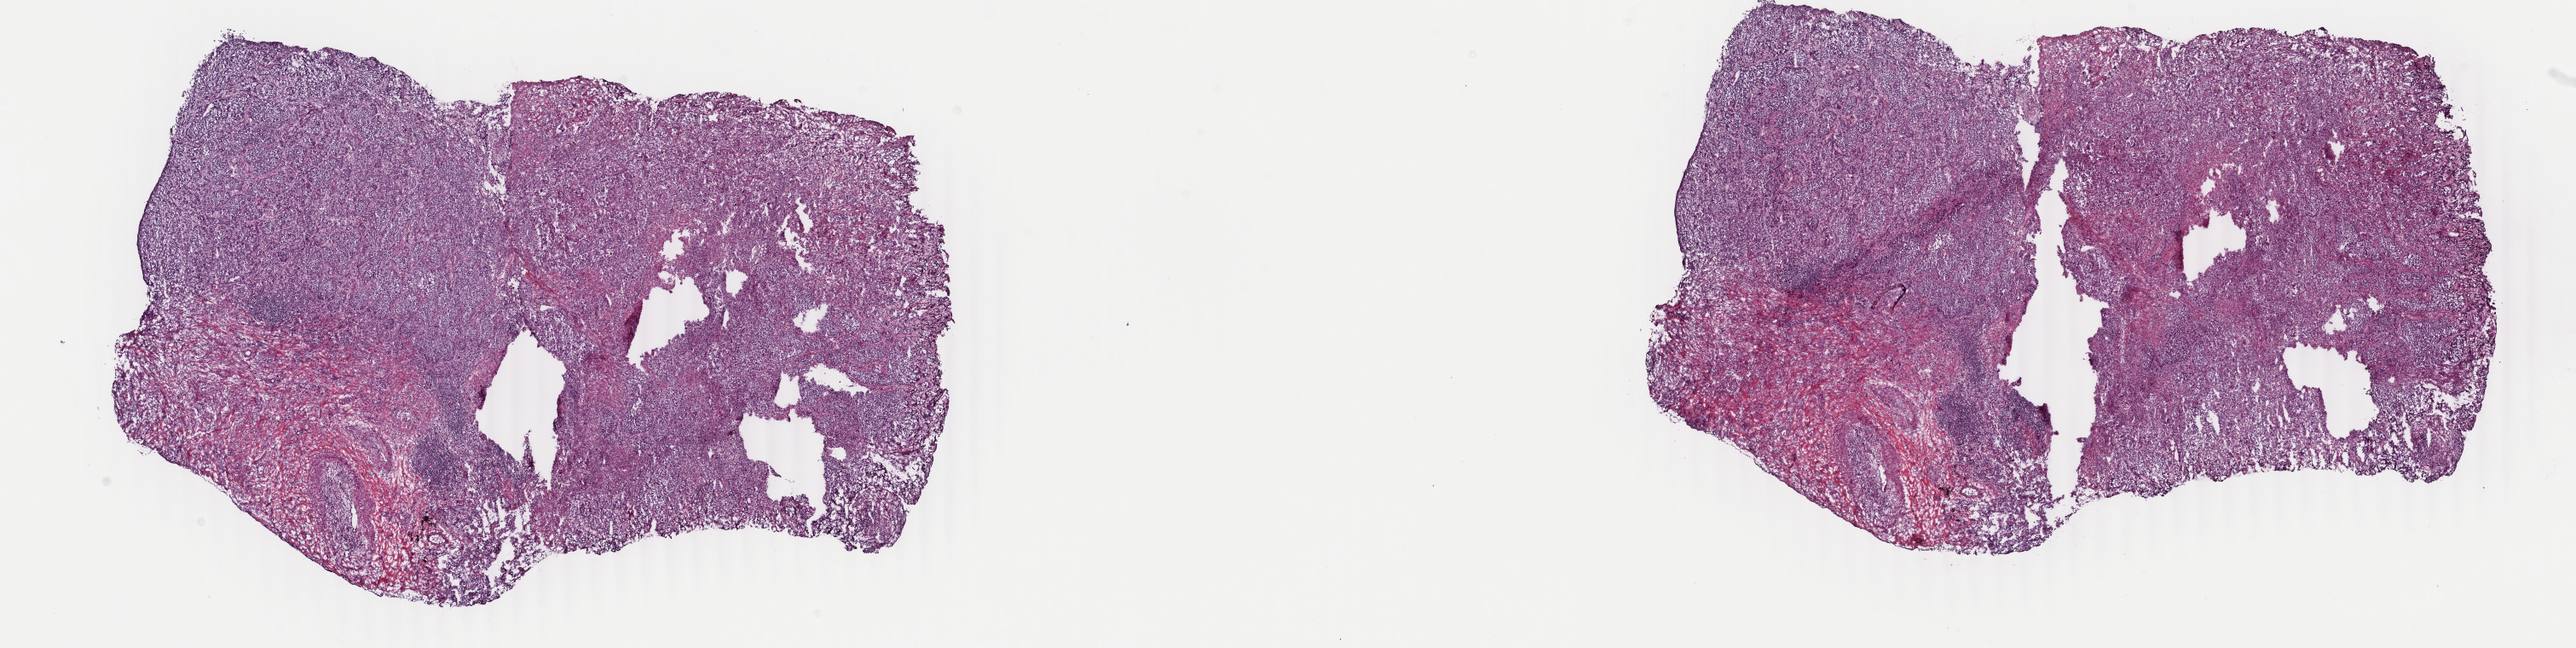
Digitized H&E tissue section (whole slide) — a low-resolution overview of the entire scanned area, about 24.0 x 6.0 mm (acquisition: 40x scan); frozen section from the top of the tissue portion; sample: primary tumour, lung. Male, age 74 years at initial diagnosis. Pathologist review of this section (percent, as recorded): tumour cells 65%, tumour nuclei 65%, normal cells 0%, stromal cells 33%, necrosis 2%. Infiltration values recorded for this section: lymphocyte infiltration 5%, monocyte infiltration 2%, neutrophil infiltration 5%.
• pathologic diagnosis: Squamous cell carcinoma, NOS (upper lobe, lung)
• AJCC pathologic stage: IIB
• TNM: T3 N0 M0